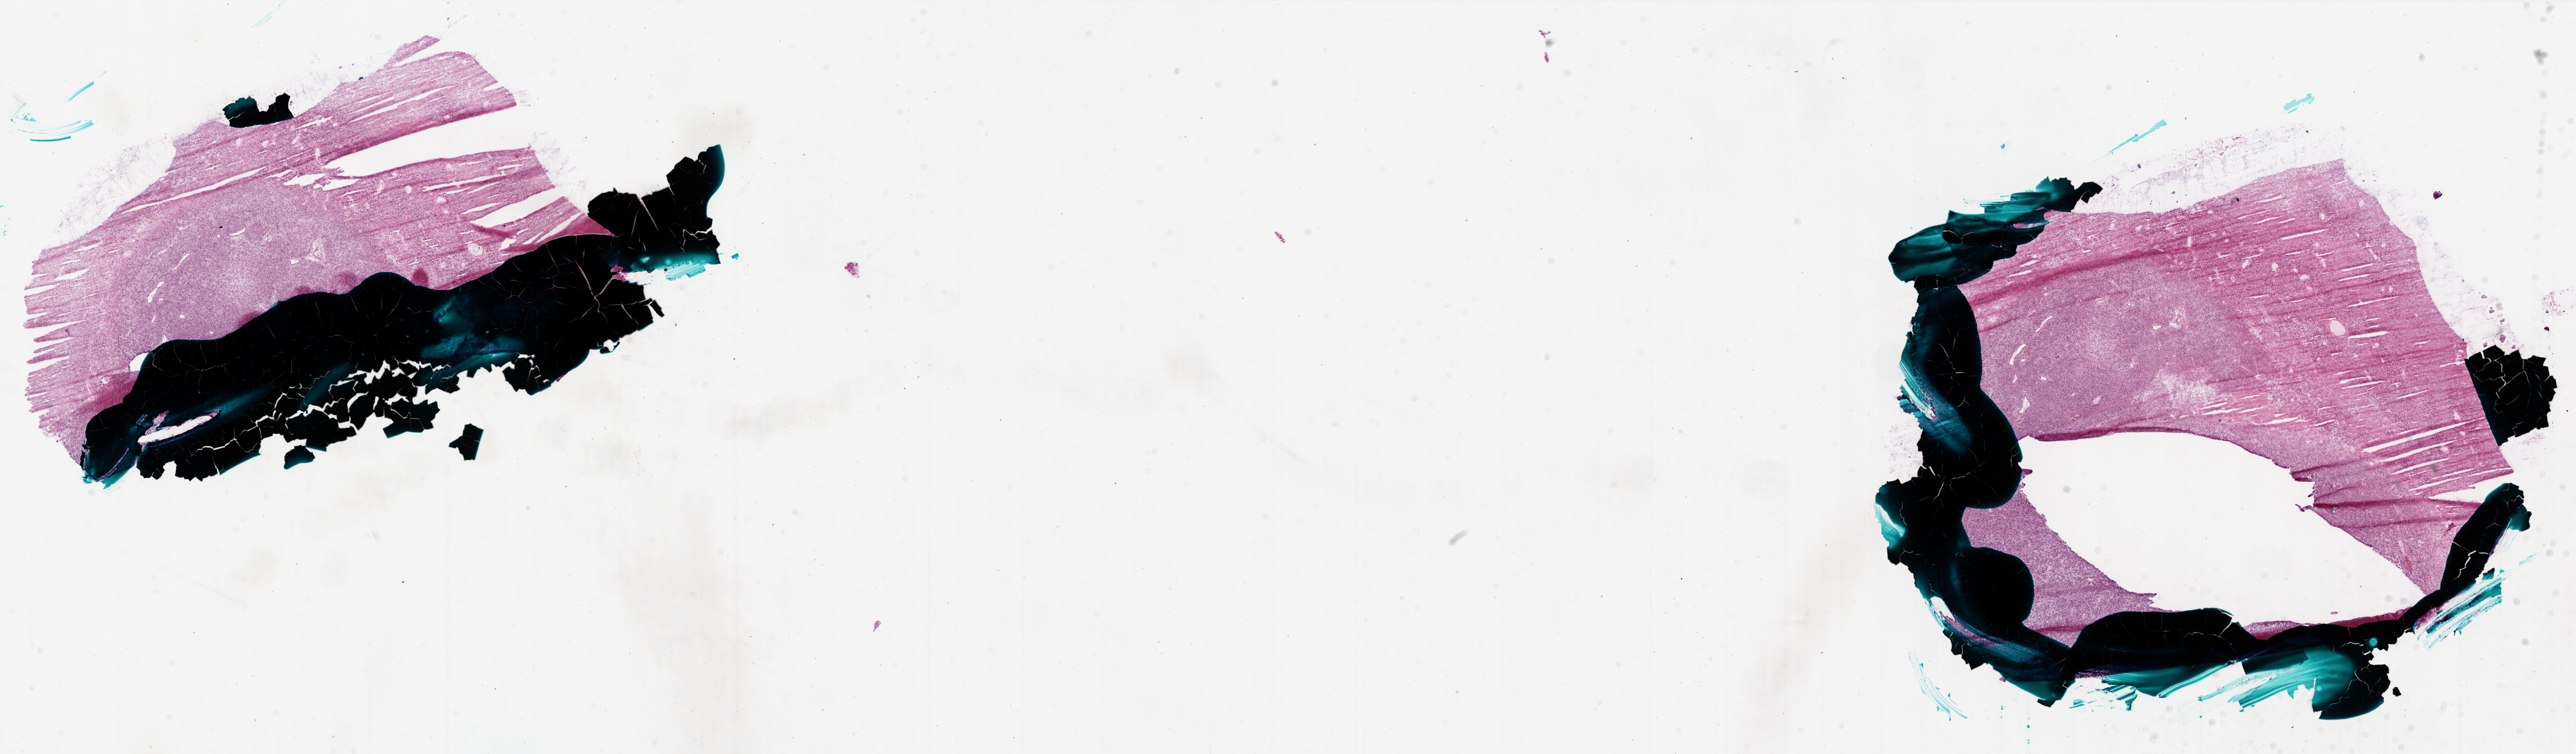
H&E-stained whole-slide image — a low-resolution overview of the entire scanned area, about 35.0 x 10.2 mm (slide scanned at 20x), frozen section, primary tumour sample from the brain. Male, age 76 years at initial diagnosis. Pathologist review of this section (percent, as recorded): tumour cells 50%, tumour nuclei 100%, normal cells 0%, stromal cells 0%, necrosis 50%. Infiltration values recorded for this section: lymphocyte infiltration 0%, monocyte infiltration 0%, neutrophil infiltration 0%.
* histologic diagnosis: Glioblastoma